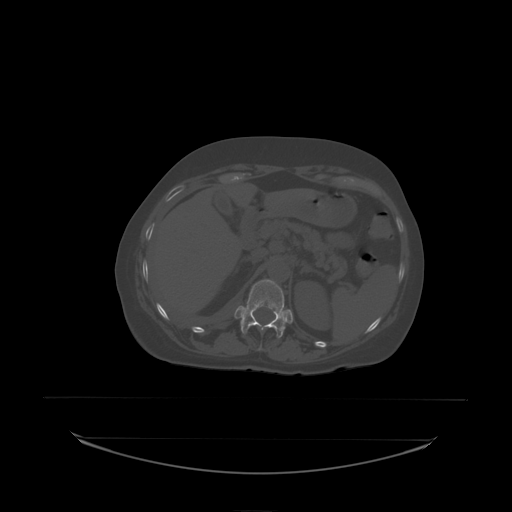
CT including the spine, one axial slice. Slice 95 of 242 in the series (ordered by position). Bone window (W 1800 / L 400 HU). 2.5 mm slice thickness. 512 × 512 image matrix, field of view 500 × 500 mm. Patient: female, 53 years. Case-level facts recorded for this patient, not image findings: primary cancer: lung; vertebrae with lytic lesions (as recorded): T7, L1.
Annotated regions visible in this slice (semi-automatically segmented with operator editing):
- T12 vertebra: box from (x=241, y=280) to (x=286, y=335) px